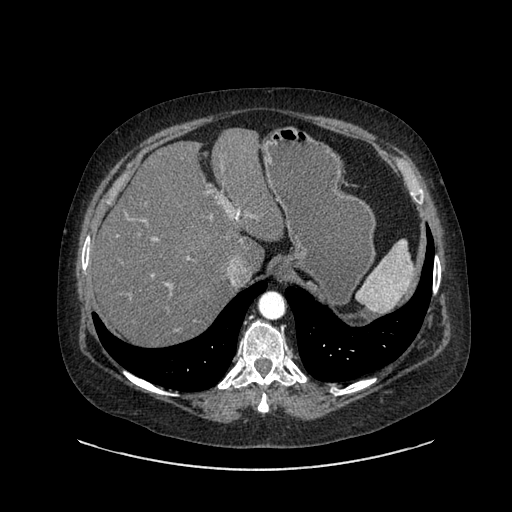
Contrast-enhanced abdominal CT, one axial slice. Position 650 of 769 along the scan axis. Soft-tissue window (W 400 / L 40 HU). 0.62 mm slice thickness. 512 × 512 image matrix, field of view 460 × 460 mm. Patient: female, 61 years. From the clinical record (not read from this slice): diagnosis: adrenocortical carcinoma; tumour side: left adrenal; tumour size at pathology: 13 cm; Ki-67 index: 79 %; stage (as recorded): 2.
Annotated regions visible in this slice (semi-automatically segmented with operator editing):
- mass: bounding box [x1, y1, x2, y2] px = [345, 312, 360, 323]